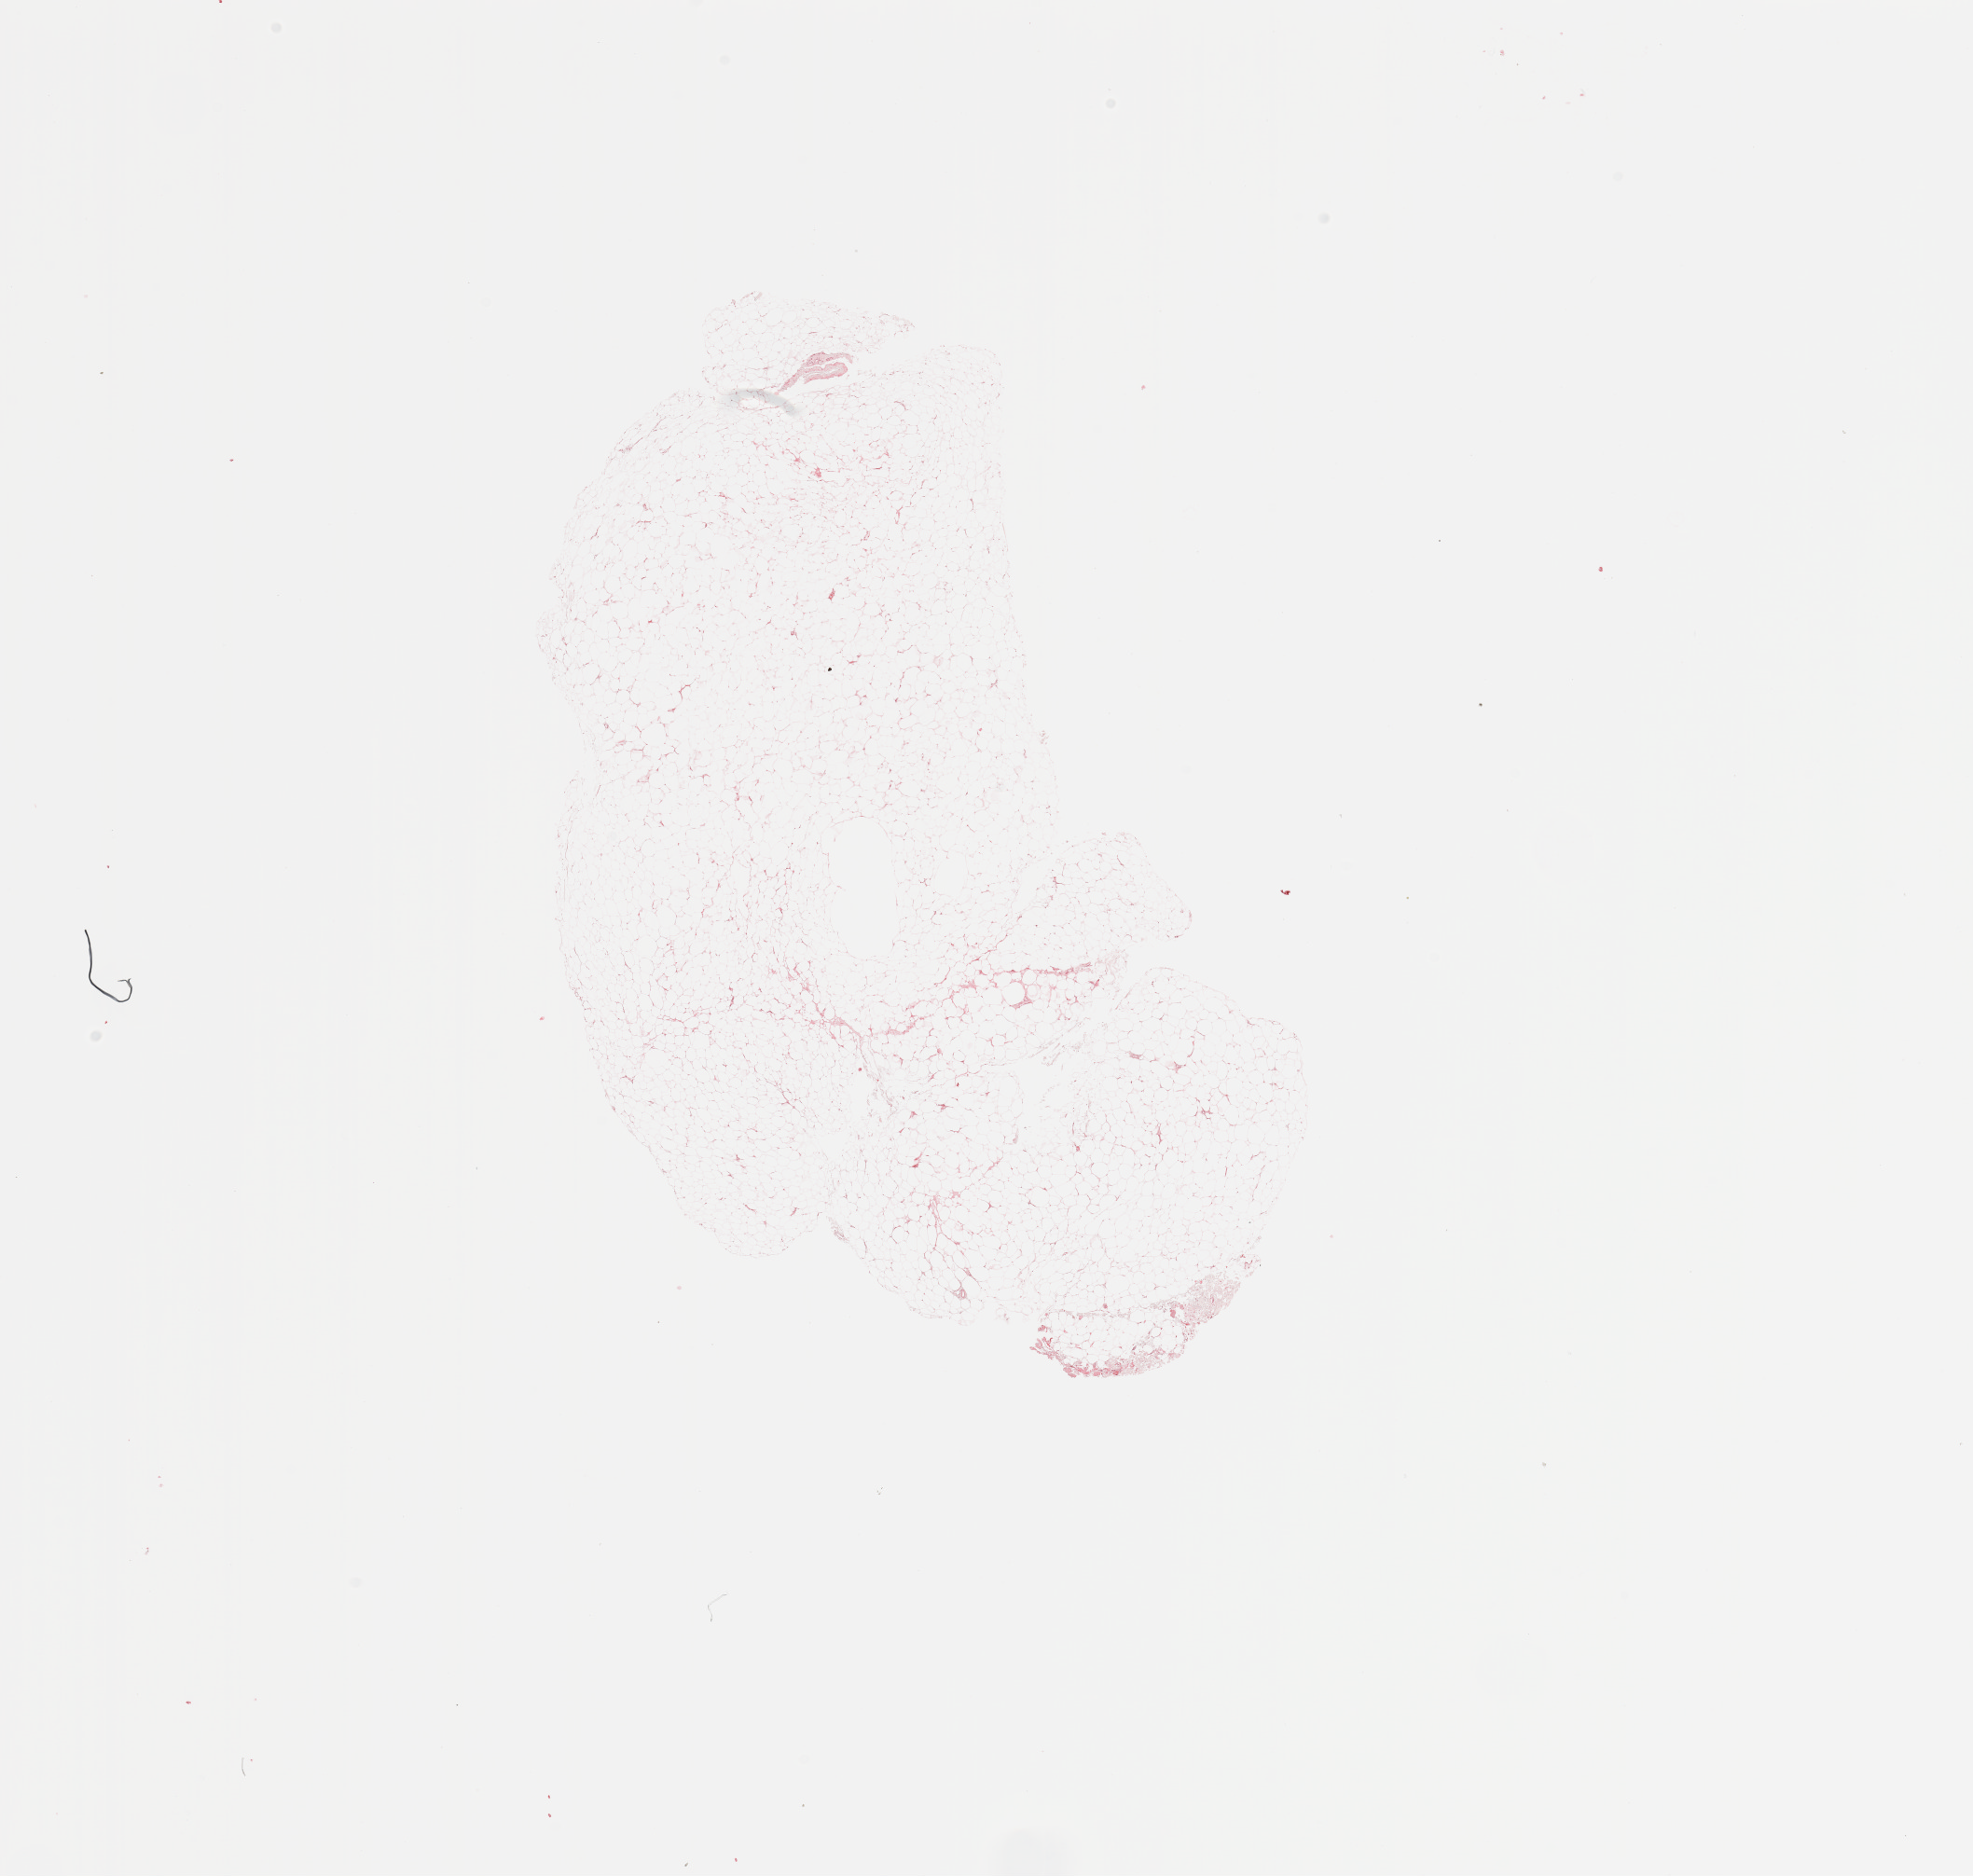
Whole-slide histology image, Hematoxylin and eosin (H&E) stained, a low-resolution overview of the entire scanned area, about 16.7 x 15.9 mm (slide scanned at 20x), kidney, normal (non-tumour) tissue. Patient: male, age 44 years.
This section: normal (non-tumour) tissue from the same patient. Patient diagnosis: Renal cell carcinoma, NOS.